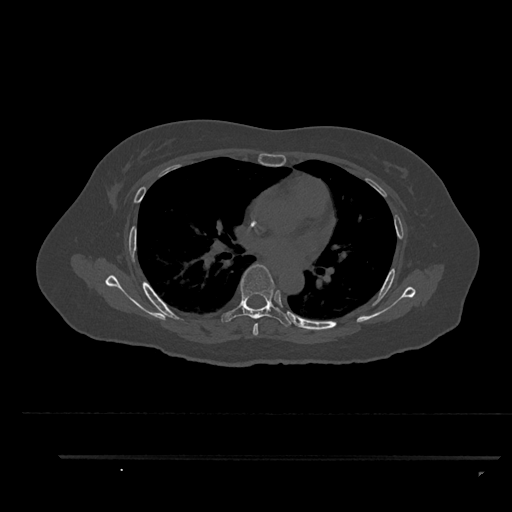
CT including the spine, one axial slice; position 565 of 797 along the scan axis; bone window (W 1800 / L 400 HU); 0.5 mm slice thickness; 512 × 512 image matrix. Female patient, age 44 years. Case-level facts recorded for this patient, not image findings: primary cancer: renal.
Structures marked on this image (semi-automatically segmented with operator editing):
- T5 vertebra: bounding box <253,323,258,336> (left, top, right, bottom; pixels)
- T6 vertebra: <221,264,294,327>